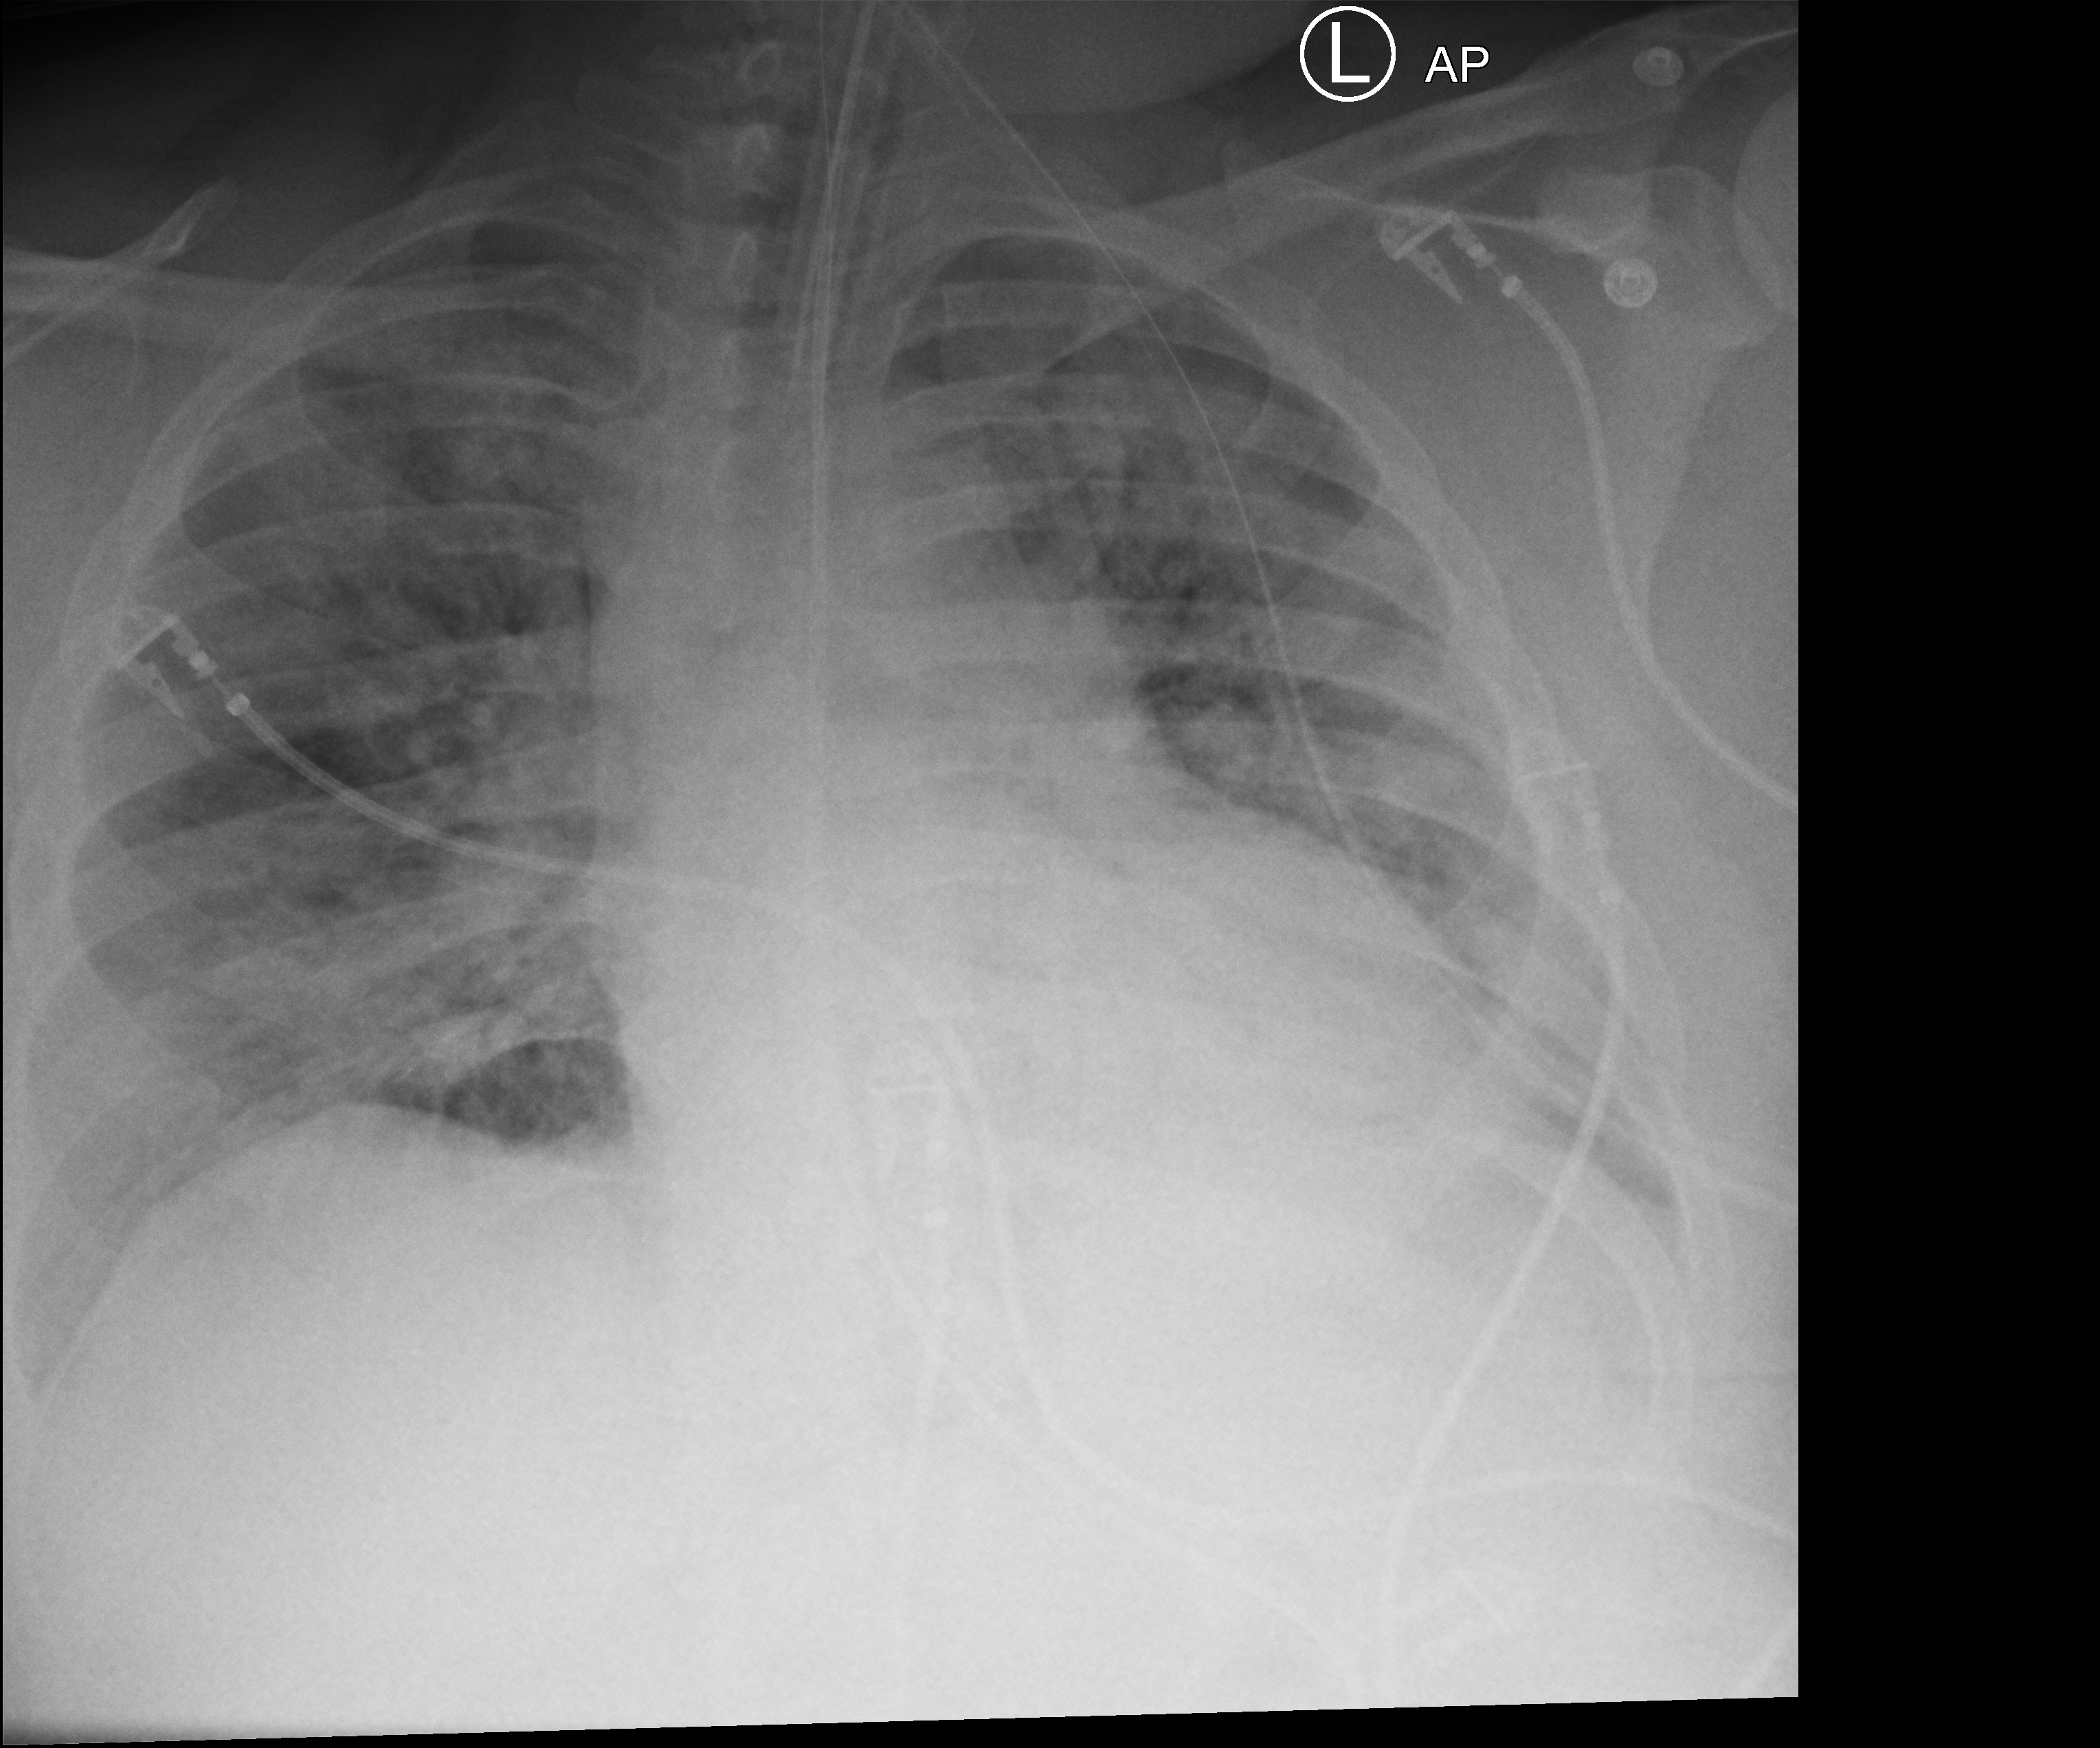
Portable chest radiograph; anteroposterior (AP) projection. Adult patient hospitalised with COVID-19, age 18–59 years.
From the hospital-stay record, not from the radiograph (when in the stay this image was taken is not recorded):
- mechanically ventilated during this hospital stay: yes
- diabetes (admission record): yes
- admitted to intensive care during this hospital stay: yes